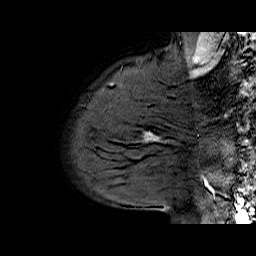
Breast MRI (dynamic contrast-enhanced), one sagittal slice. Position 54 of 70 along the scan axis. Dynamic contrast-enhanced series, time point 2 of 6 at this slice position (early post-contrast). 1.5 T. TE 6.5 ms, TR 33 ms. 4 mm slice thickness. 256 × 256 image matrix, field of view 200 × 200 mm. Female patient. From the clinical record (not read from this slice): setting: breast cancer imaged before/during neoadjuvant chemotherapy; receptor status: HER2-positive.
Outlined on this slice (semi-automatically segmented with operator editing):
- analysis volume of interest (the breast-tissue region the enhancement analysis was run in; not a lesion): bounding box (x1, y1, x2, y2) in pixels: (113, 112, 174, 170)
- tumour enhancement mask (voxels above the 100 % enhancement threshold inside the analysis volume of interest): (144, 132, 152, 139)